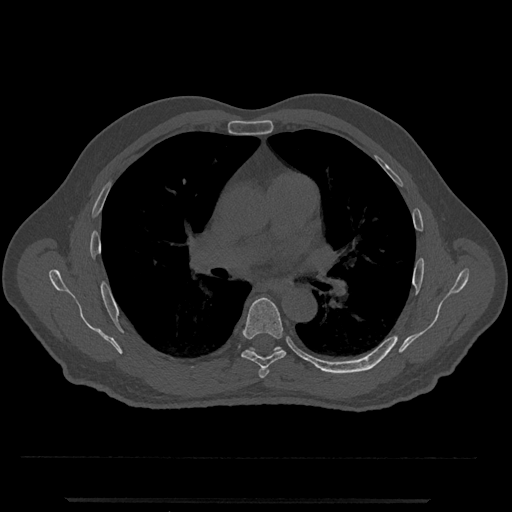
CT including the spine, one axial slice; reconstruction kernel Br40s/3; bone window (W 1800 / L 400 HU); 512 × 512 image matrix, field of view 419 × 419 mm. Male patient, age 63 years. Case-level facts recorded for this patient, not image findings: primary cancer: prostate.
Outlined on this slice (semi-automatic segmentation, software-assisted and operator-edited):
- T5 vertebra: box from (x=258, y=368) to (x=269, y=378) px
- T6 vertebra: (x=241, y=297)–(x=286, y=369)
- T7 vertebra: (x=249, y=346)–(x=322, y=371)